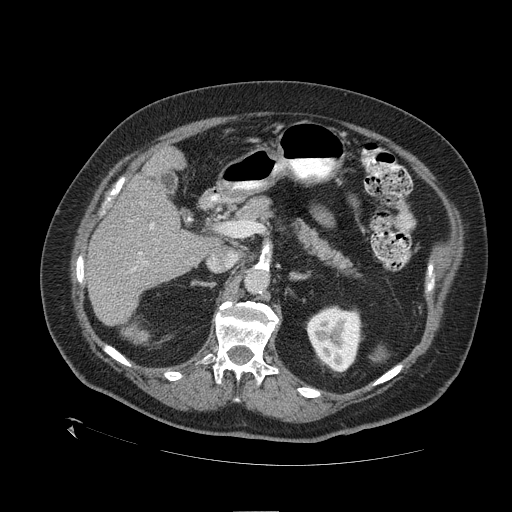
Contrast-enhanced abdominal CT (liver protocol), one axial slice; position 61 of 109 along the scan axis; reconstruction kernel STANDARD; 120 kVp; one of 2 acquisitions stored at this slice position; soft-tissue window (W 400 / L 40 HU); 512 × 512 image matrix. Case-level facts recorded for this patient, not image findings: diagnosis: hepatocellular carcinoma (patient treated with transarterial chemoembolisation; whether this scan precedes or follows treatment is not stated here); TNM stage (as recorded): Stage-I; Child-Pugh class: A; tumour differentiation: no biopsy; tumour nodularity: uninodular.
Outlined on this slice (semi-automatically segmented with operator editing):
- liver parenchyma outside the tumour (the mass and vessels are separate outlines, so this box may not span the whole liver): bounding box [x1, y1, x2, y2] px = [88, 152, 214, 324]
- liver vessels: [132, 223, 154, 271]